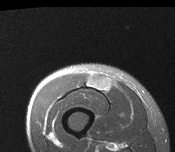
MRI of an extremity soft-tissue mass, one axial slice; position 35 of 116 along the scan axis; T2-weighted fat-saturated; MR volume resampled by the dataset authors to the PET/CT grid (not the native acquisition matrix); 175 × 152 image matrix. Male patient. From the clinical record (not read from this slice): histological type: pleiomorphic leiomyosarcoma; grade: intermediate; site of the primary tumour: right thigh.
Outlined on this slice (expert contour drawn on MRI and transferred to this co-registered scan by the dataset authors):
- gross tumour volume including surrounding oedema: box from (x=86, y=74) to (x=110, y=93) px